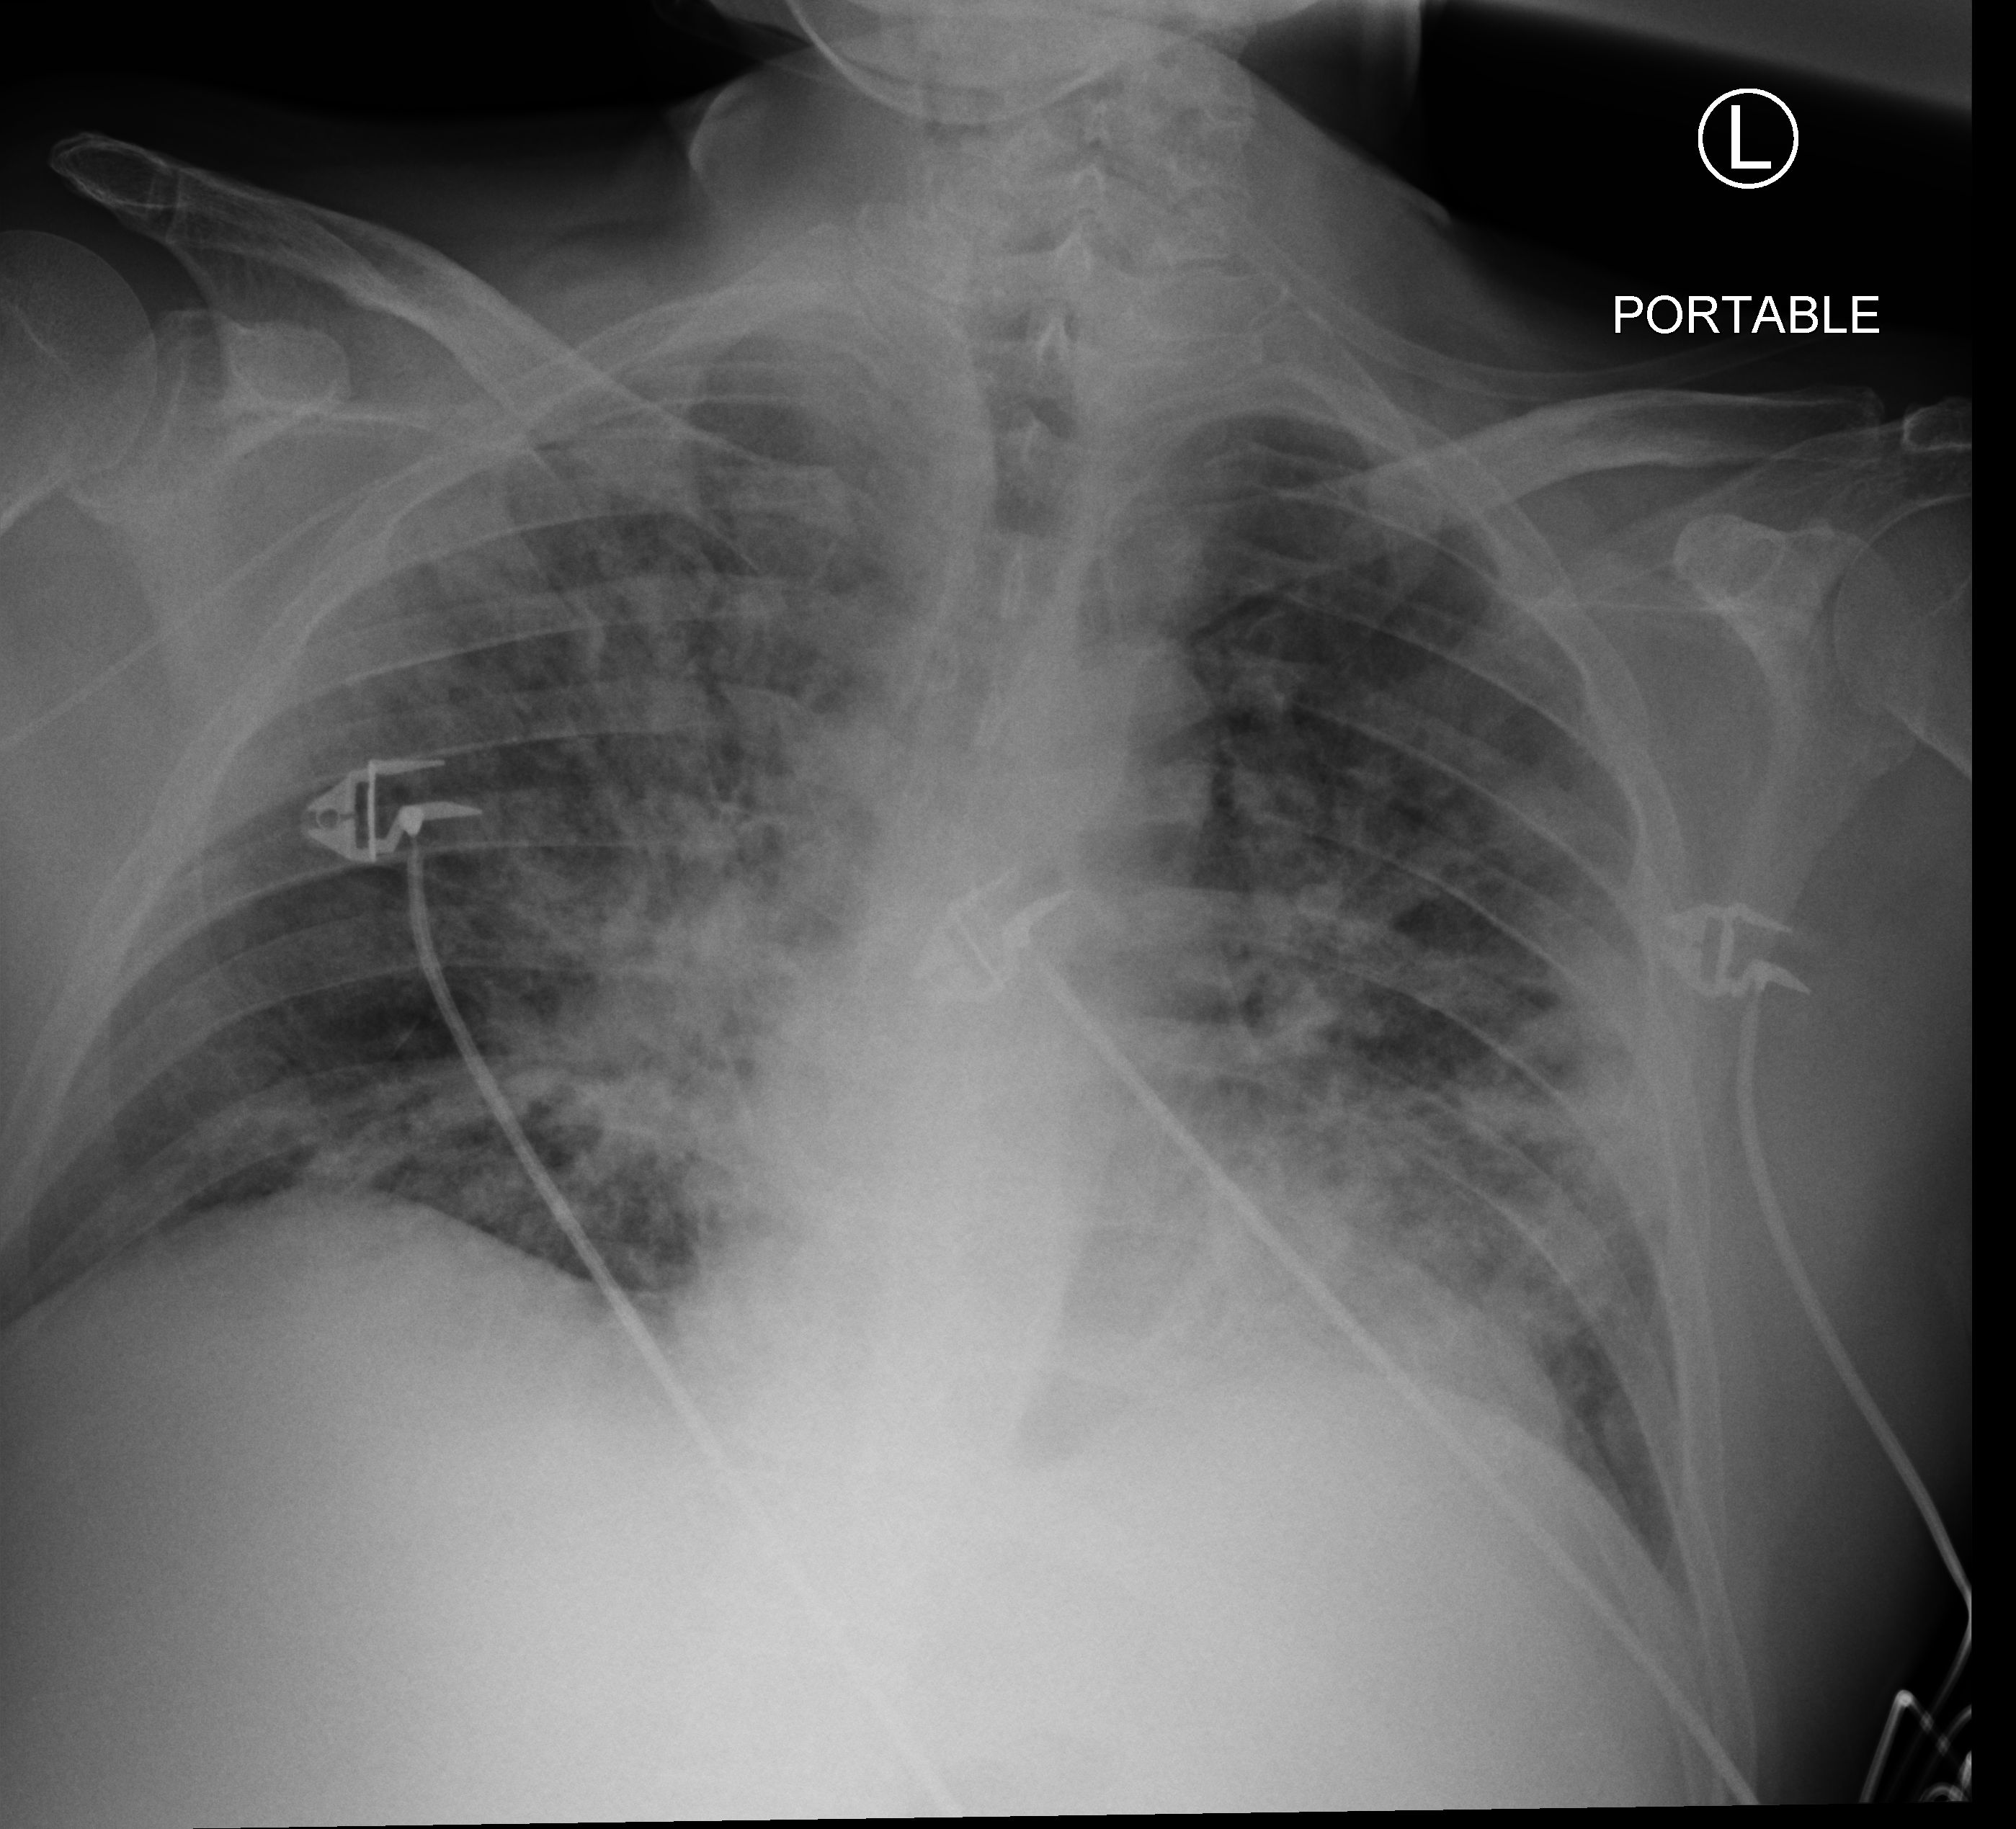
Portable chest radiograph; anteroposterior (AP) projection. Patient hospitalised with COVID-19; male, aged 60–74 years.
Admission-level facts for this patient (not findings on this image; timing relative to this image not recorded):
- length of hospital stay: 24 days
- COPD (admission record): no
- admitted to intensive care during this hospital stay: yes